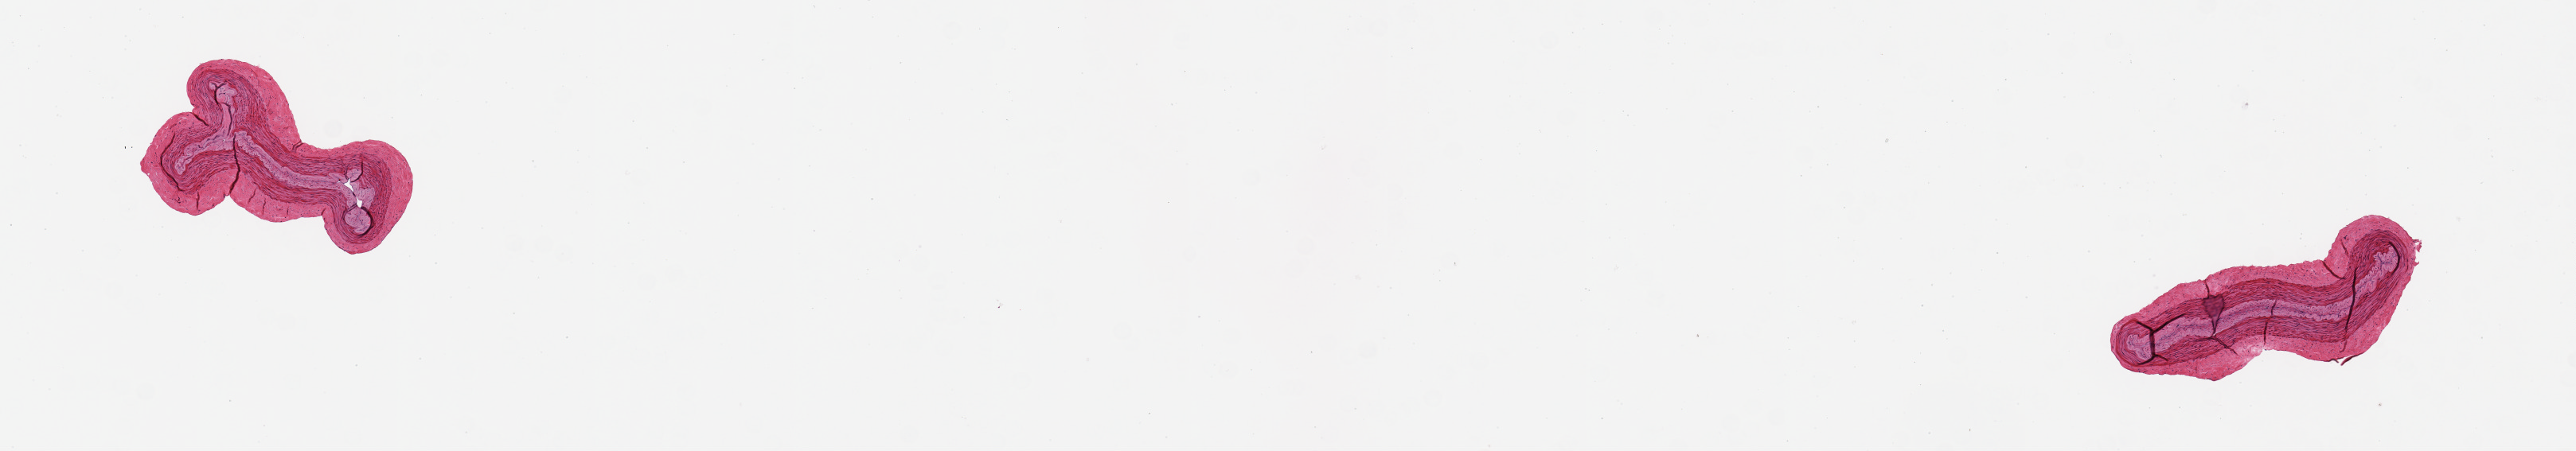
Whole-slide image, hematoxylin and eosin (H&E) stain, shown as a low-resolution overview of the whole scanned area (about 12.8 x 2.2 mm). PAXgene-fixed, paraffin-embedded tissue. Target tissue: tibial artery. Donor tissue sample. Male donor.
Reviewer comment on this tissue sample: 2 pieces, small muscular artery.